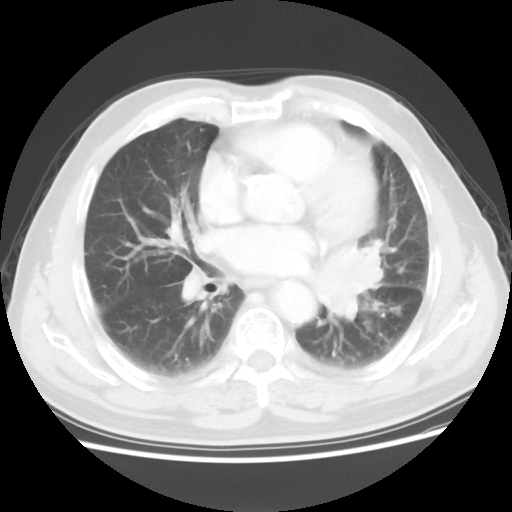
Chest CT, one axial slice; position 29 of 56 along the scan axis; reconstruction kernel STANDARD; 120 kVp; lung window (W 1500 / L -600 HU); 512 × 512 image matrix, field of view 360 × 360 mm. Male patient, age 75 years. From the clinical record (not read from this slice): clinical TNM (as recorded): T3 N0 M0.
Structures marked on this image (bounding box drawn by a radiologist):
- lung tumour (recorded histology: squamous cell carcinoma): bounding box <319,233,389,326> (left, top, right, bottom; pixels)